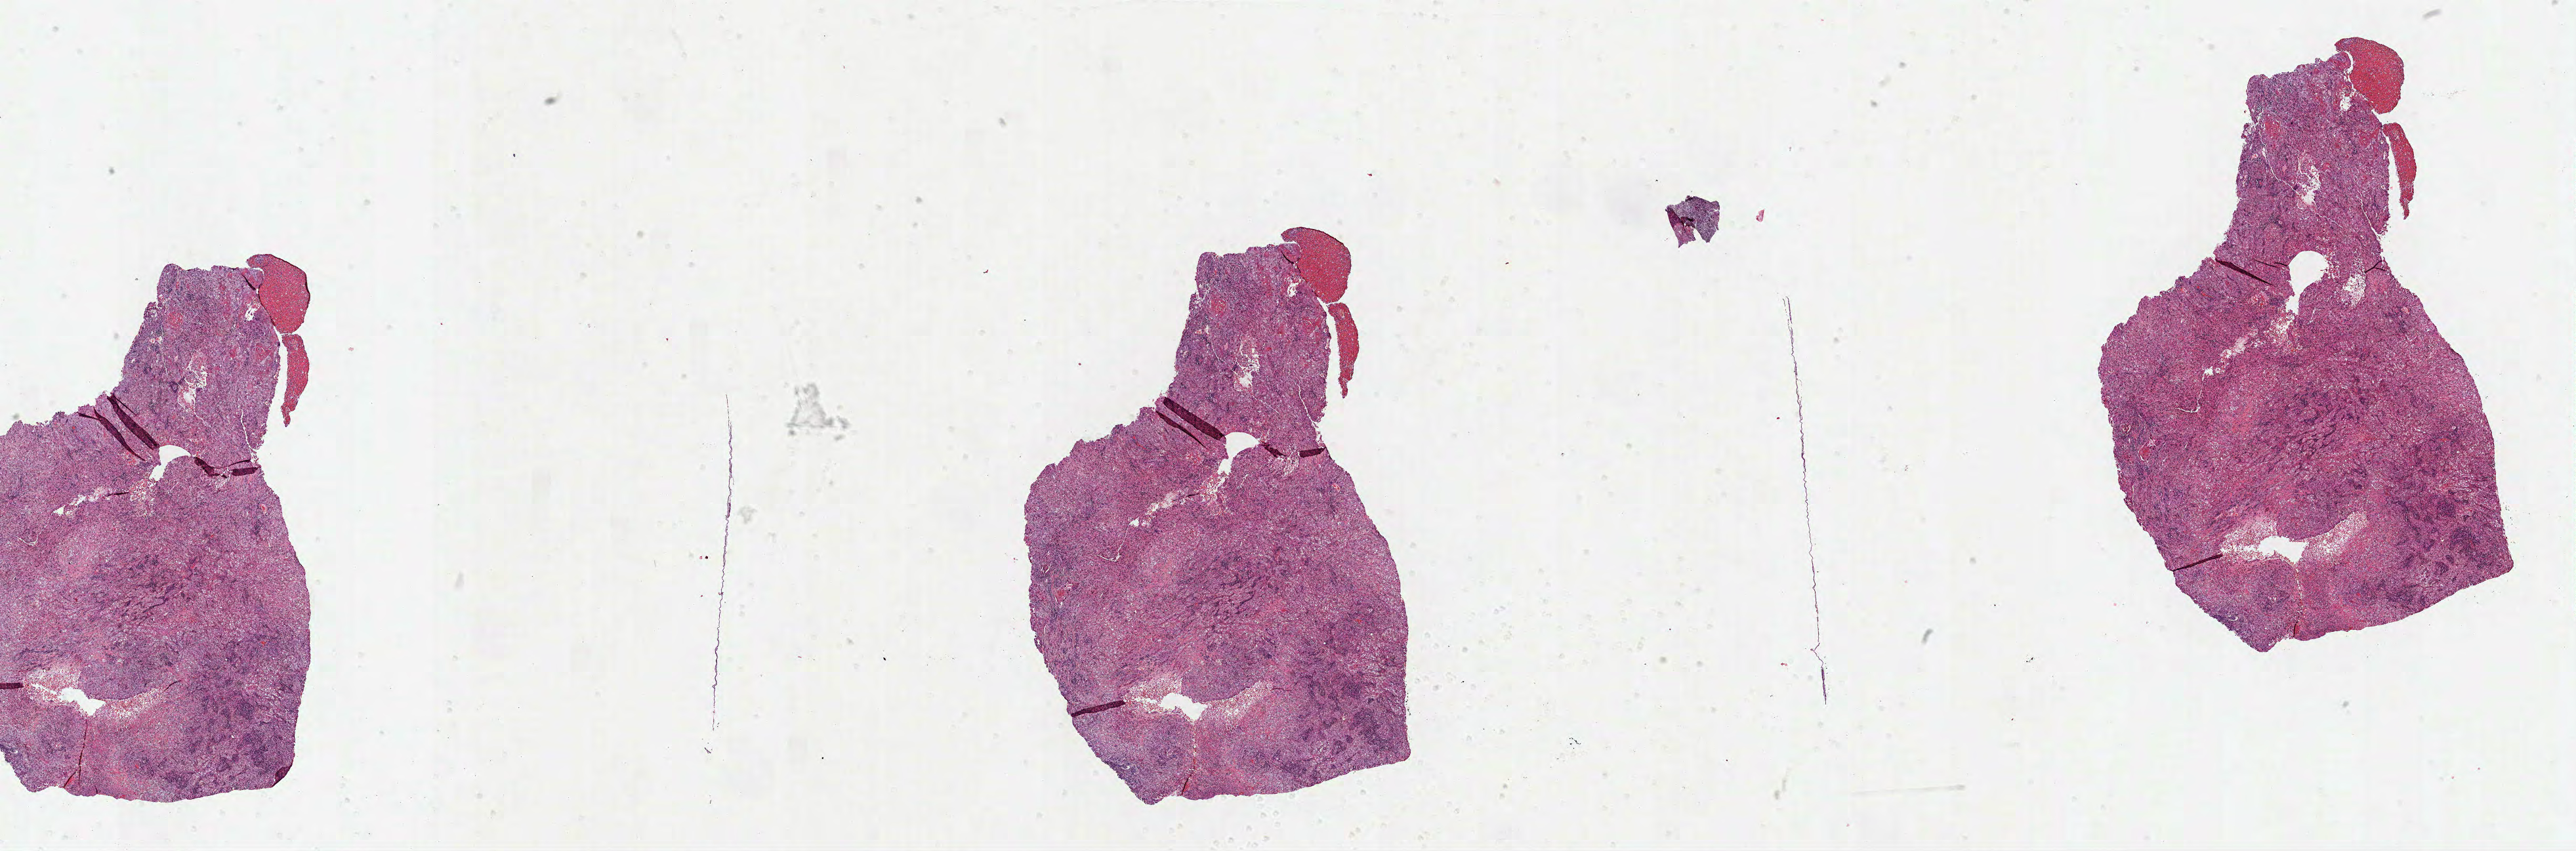
Digitized Hematoxylin and eosin (H&E) stained tissue section (whole slide) — whole scanned area (about 31.7 x 10.5 mm, acquisition: 40x scan) shown as a low-resolution overview. Formalin-fixed paraffin-embedded (FFPE) diagnostic section. Sample: primary tumour, lung. Patient: female, age at initial diagnosis 69 years.
* diagnosis: Squamous cell carcinoma, NOS
* TNM: T2b N1 MX
* laterality: right
* AJCC pathologic stage: IIB (7th edition)